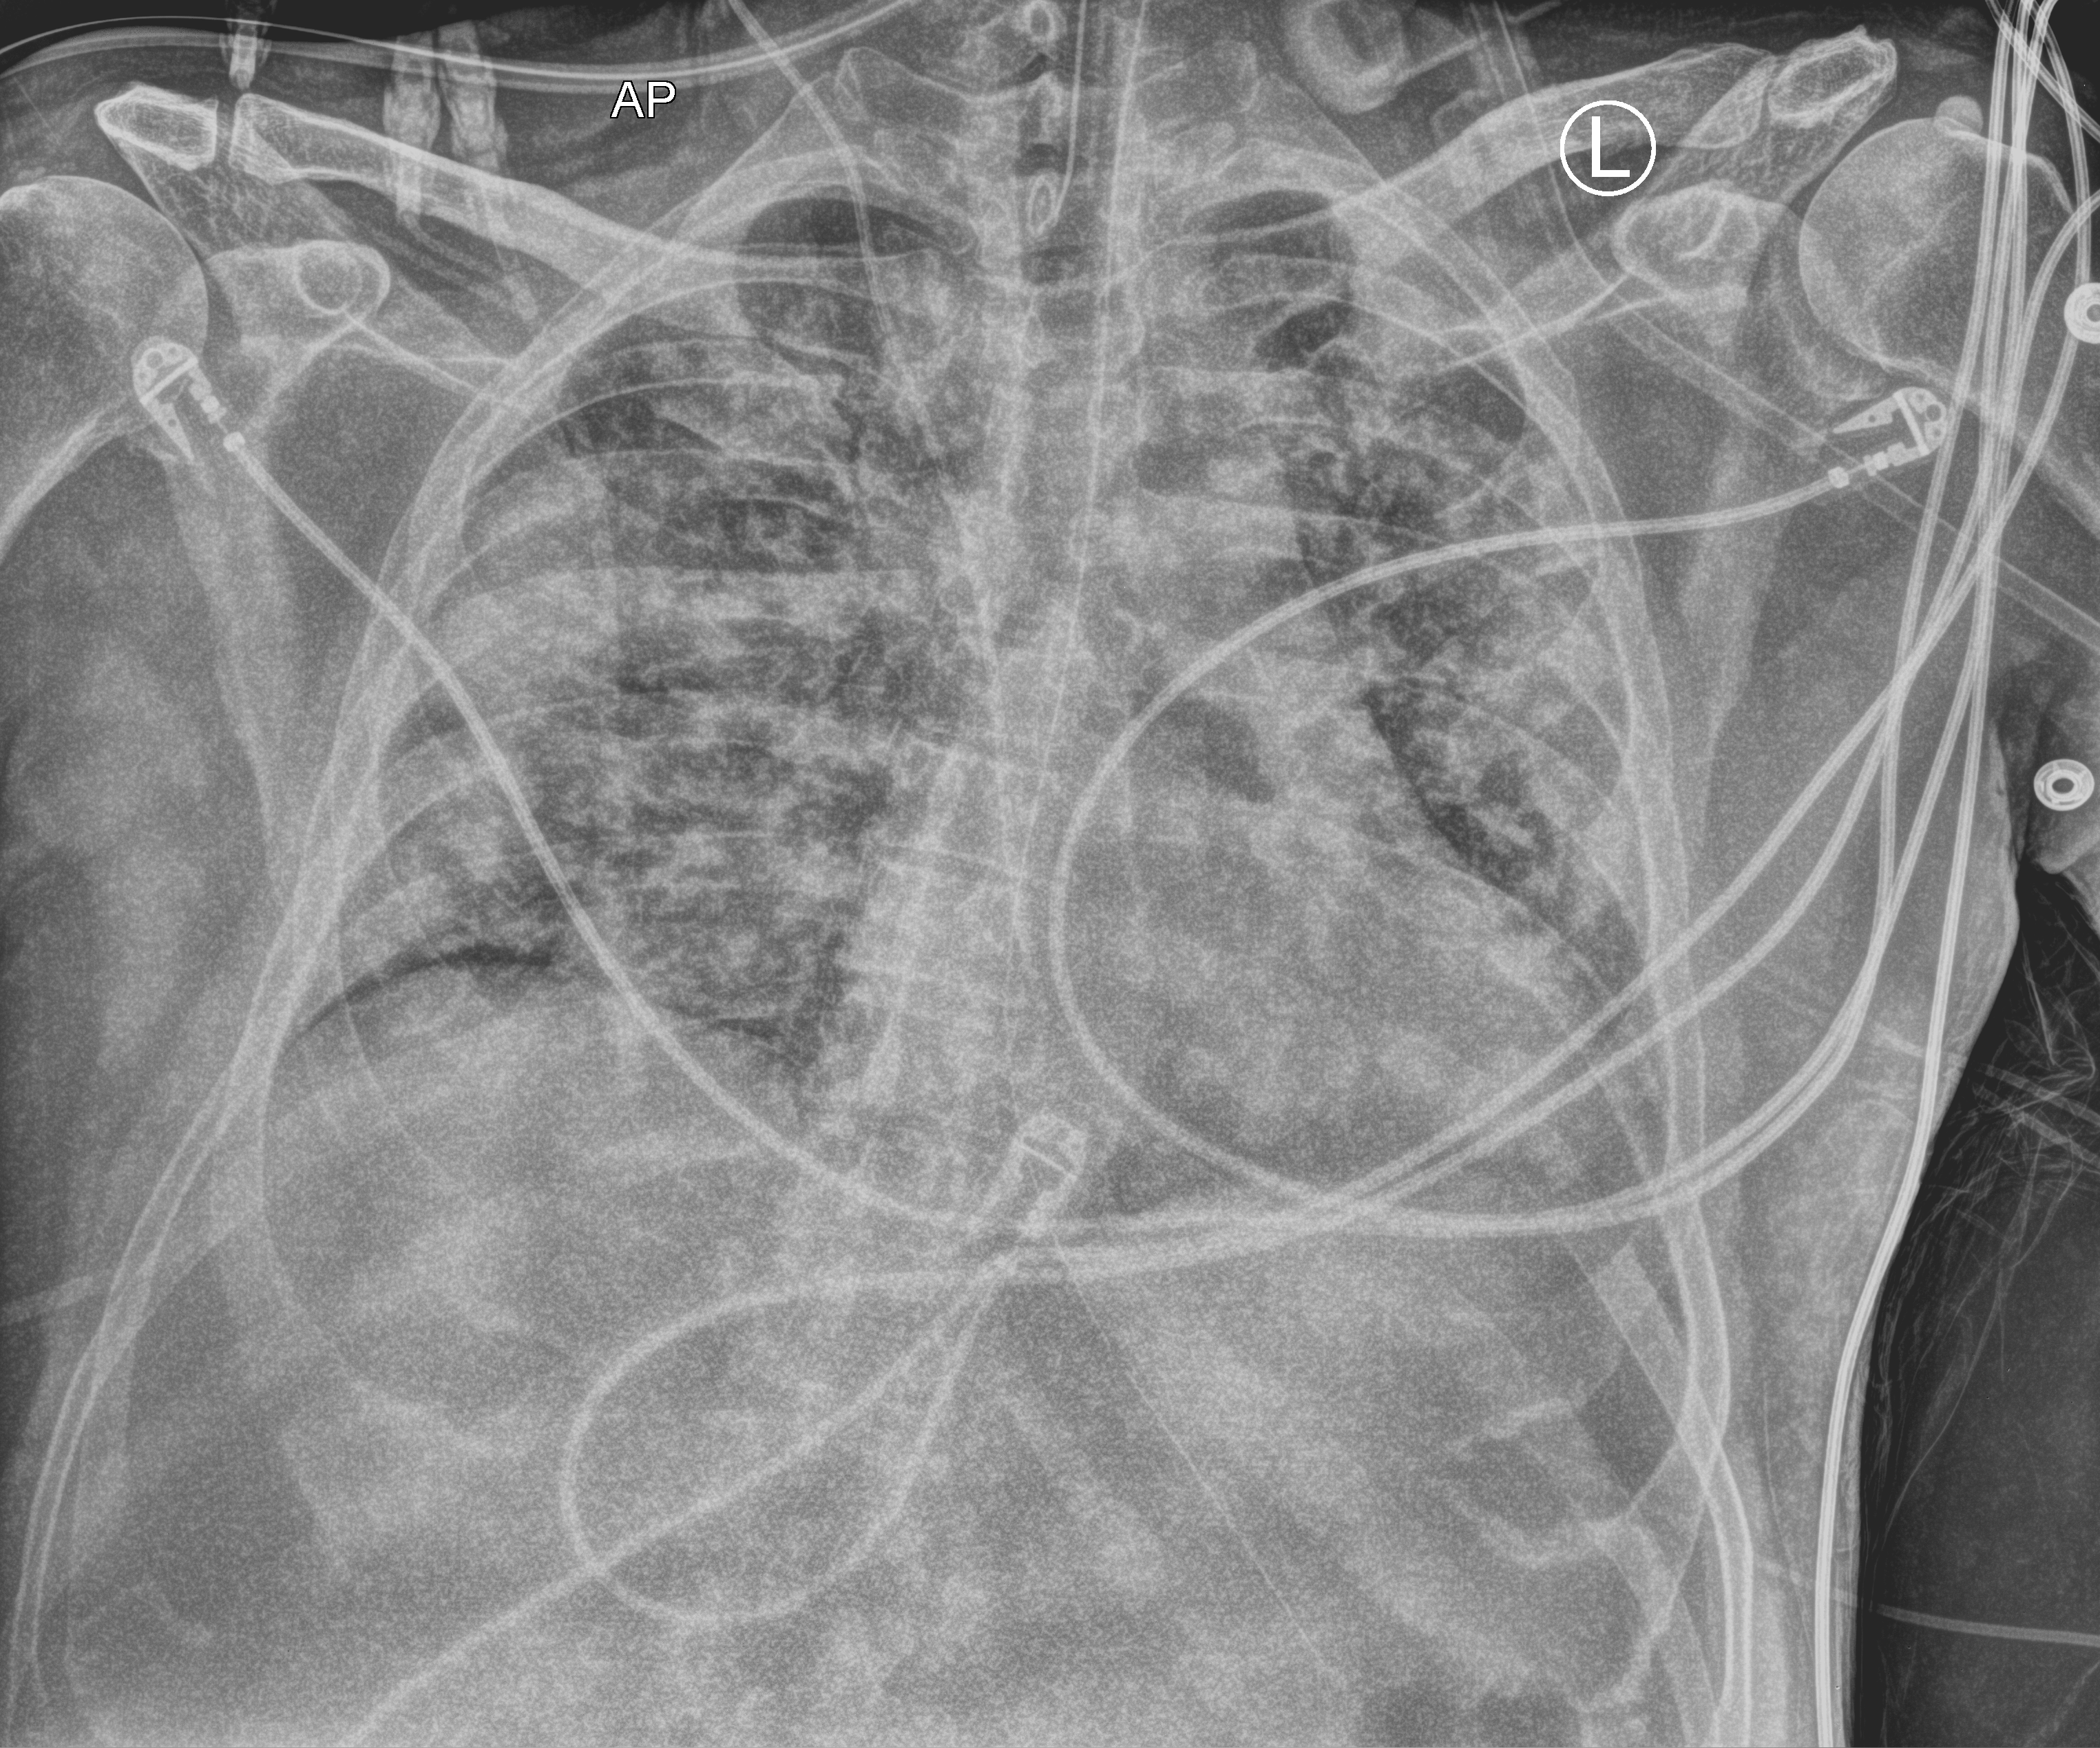
Chest X-ray (portable), anteroposterior (AP) projection. Male patient hospitalised with COVID-19, age 18–59 years.
Hospital-stay facts (about this admission, not read from this image; timing relative to this image not recorded): chronic kidney disease (admission record): no; mechanically ventilated during this hospital stay: yes.